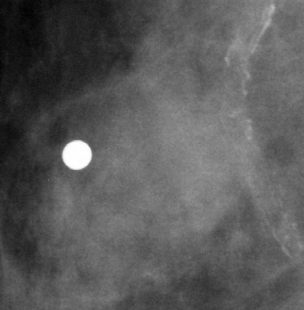
Region of interest cut from a scanned film mammogram (one marked finding), right breast, MLO view.
- Finding: mass, shape oval, margins circumscribed; BI-RADS assessment category 4; pathology (as recorded): malignant.